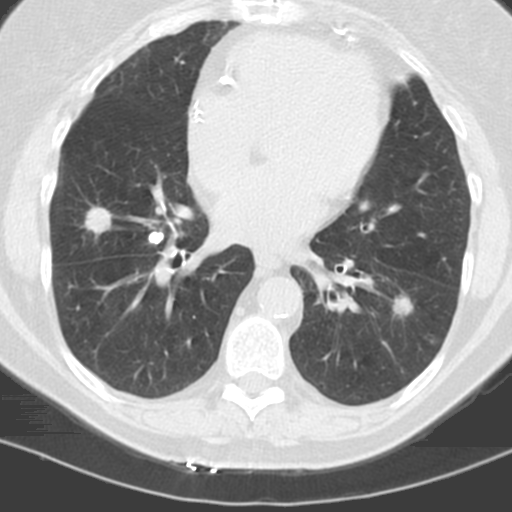
Axial slice from a low-dose chest CT screening exam; baseline screening round; lung window (W 1500 / L -600 HU); 3.2 mm slice thickness; standard (soft-tissue) reconstruction kernel (C); 120 kVp; slice 74 of 121 in the series; 512 × 512 image matrix, field of view 278 × 278 mm. Female participant, aged 60 years at enrolment. Former smoker at enrolment.
• Lesion marked by an expert reader, bounding box (x1, y1, x2, y2) in pixels: (377, 286, 423, 327).
• The screening reader recorded 3 non-calcified nodules or masses ≥4 mm on this exam; which of them this box marks is not recorded.
• Lung cancer was diagnosed 96 days after this screen: adenocarcinoma, NOS, left lower lobe, stage IV (AJCC 6th edition), 22 mm at pathology.